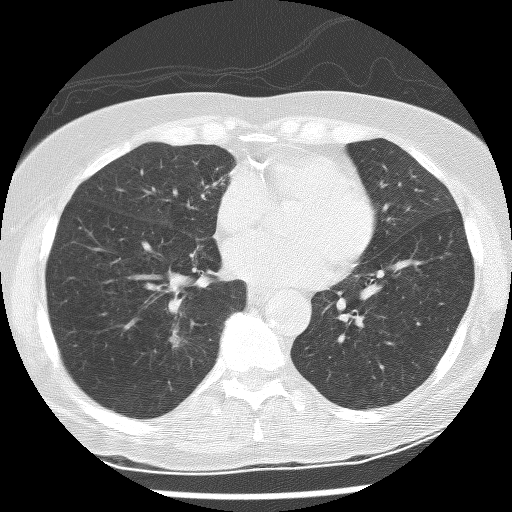
Axial slice from a low-dose chest CT screening exam; first (baseline) screen; lung window (W 1500 / L -600 HU); 2.5 mm slice thickness; lung (sharp) reconstruction kernel (BONE); slice 144 of 247 in the series; 512 × 512 image matrix. Female, age 60 years at enrolment. Former smoker at enrolment.
Expert-annotated lung lesion, bounding box (x1, y1, x2, y2) in pixels: (155, 322, 204, 358). Screening reader's record for this exam (one nodule recorded; not confirmed to be the boxed lesion): non-calcified nodule or mass ≥4 mm, right lower lobe, 10 × 6 mm, spiculated (stellate) margins, mixed attenuation. Lung cancer was diagnosed 275 days after this screen: adenocarcinoma with squamous metaplasia, right lower lobe, poorly differentiated (G3), stage IA (AJCC 6th edition), 23 mm at pathology.